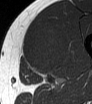
MRI of an extremity soft-tissue mass, one axial slice. Position 34 of 62 along the scan axis. MR volume resampled by the dataset authors to the PET/CT grid (not the native acquisition matrix). 3.27 mm slice thickness. 92 × 104 image matrix, field of view 90 × 102 mm. Male patient. Case-level facts recorded for this patient, not image findings: histological type: mixoid liposarcoma; grade: low; site of the primary tumour: left thigh.
Annotated regions visible in this slice (expert contour drawn on MRI and transferred to this co-registered scan by the dataset authors):
- gross tumour volume (mass): box from (x=23, y=24) to (x=70, y=77) px